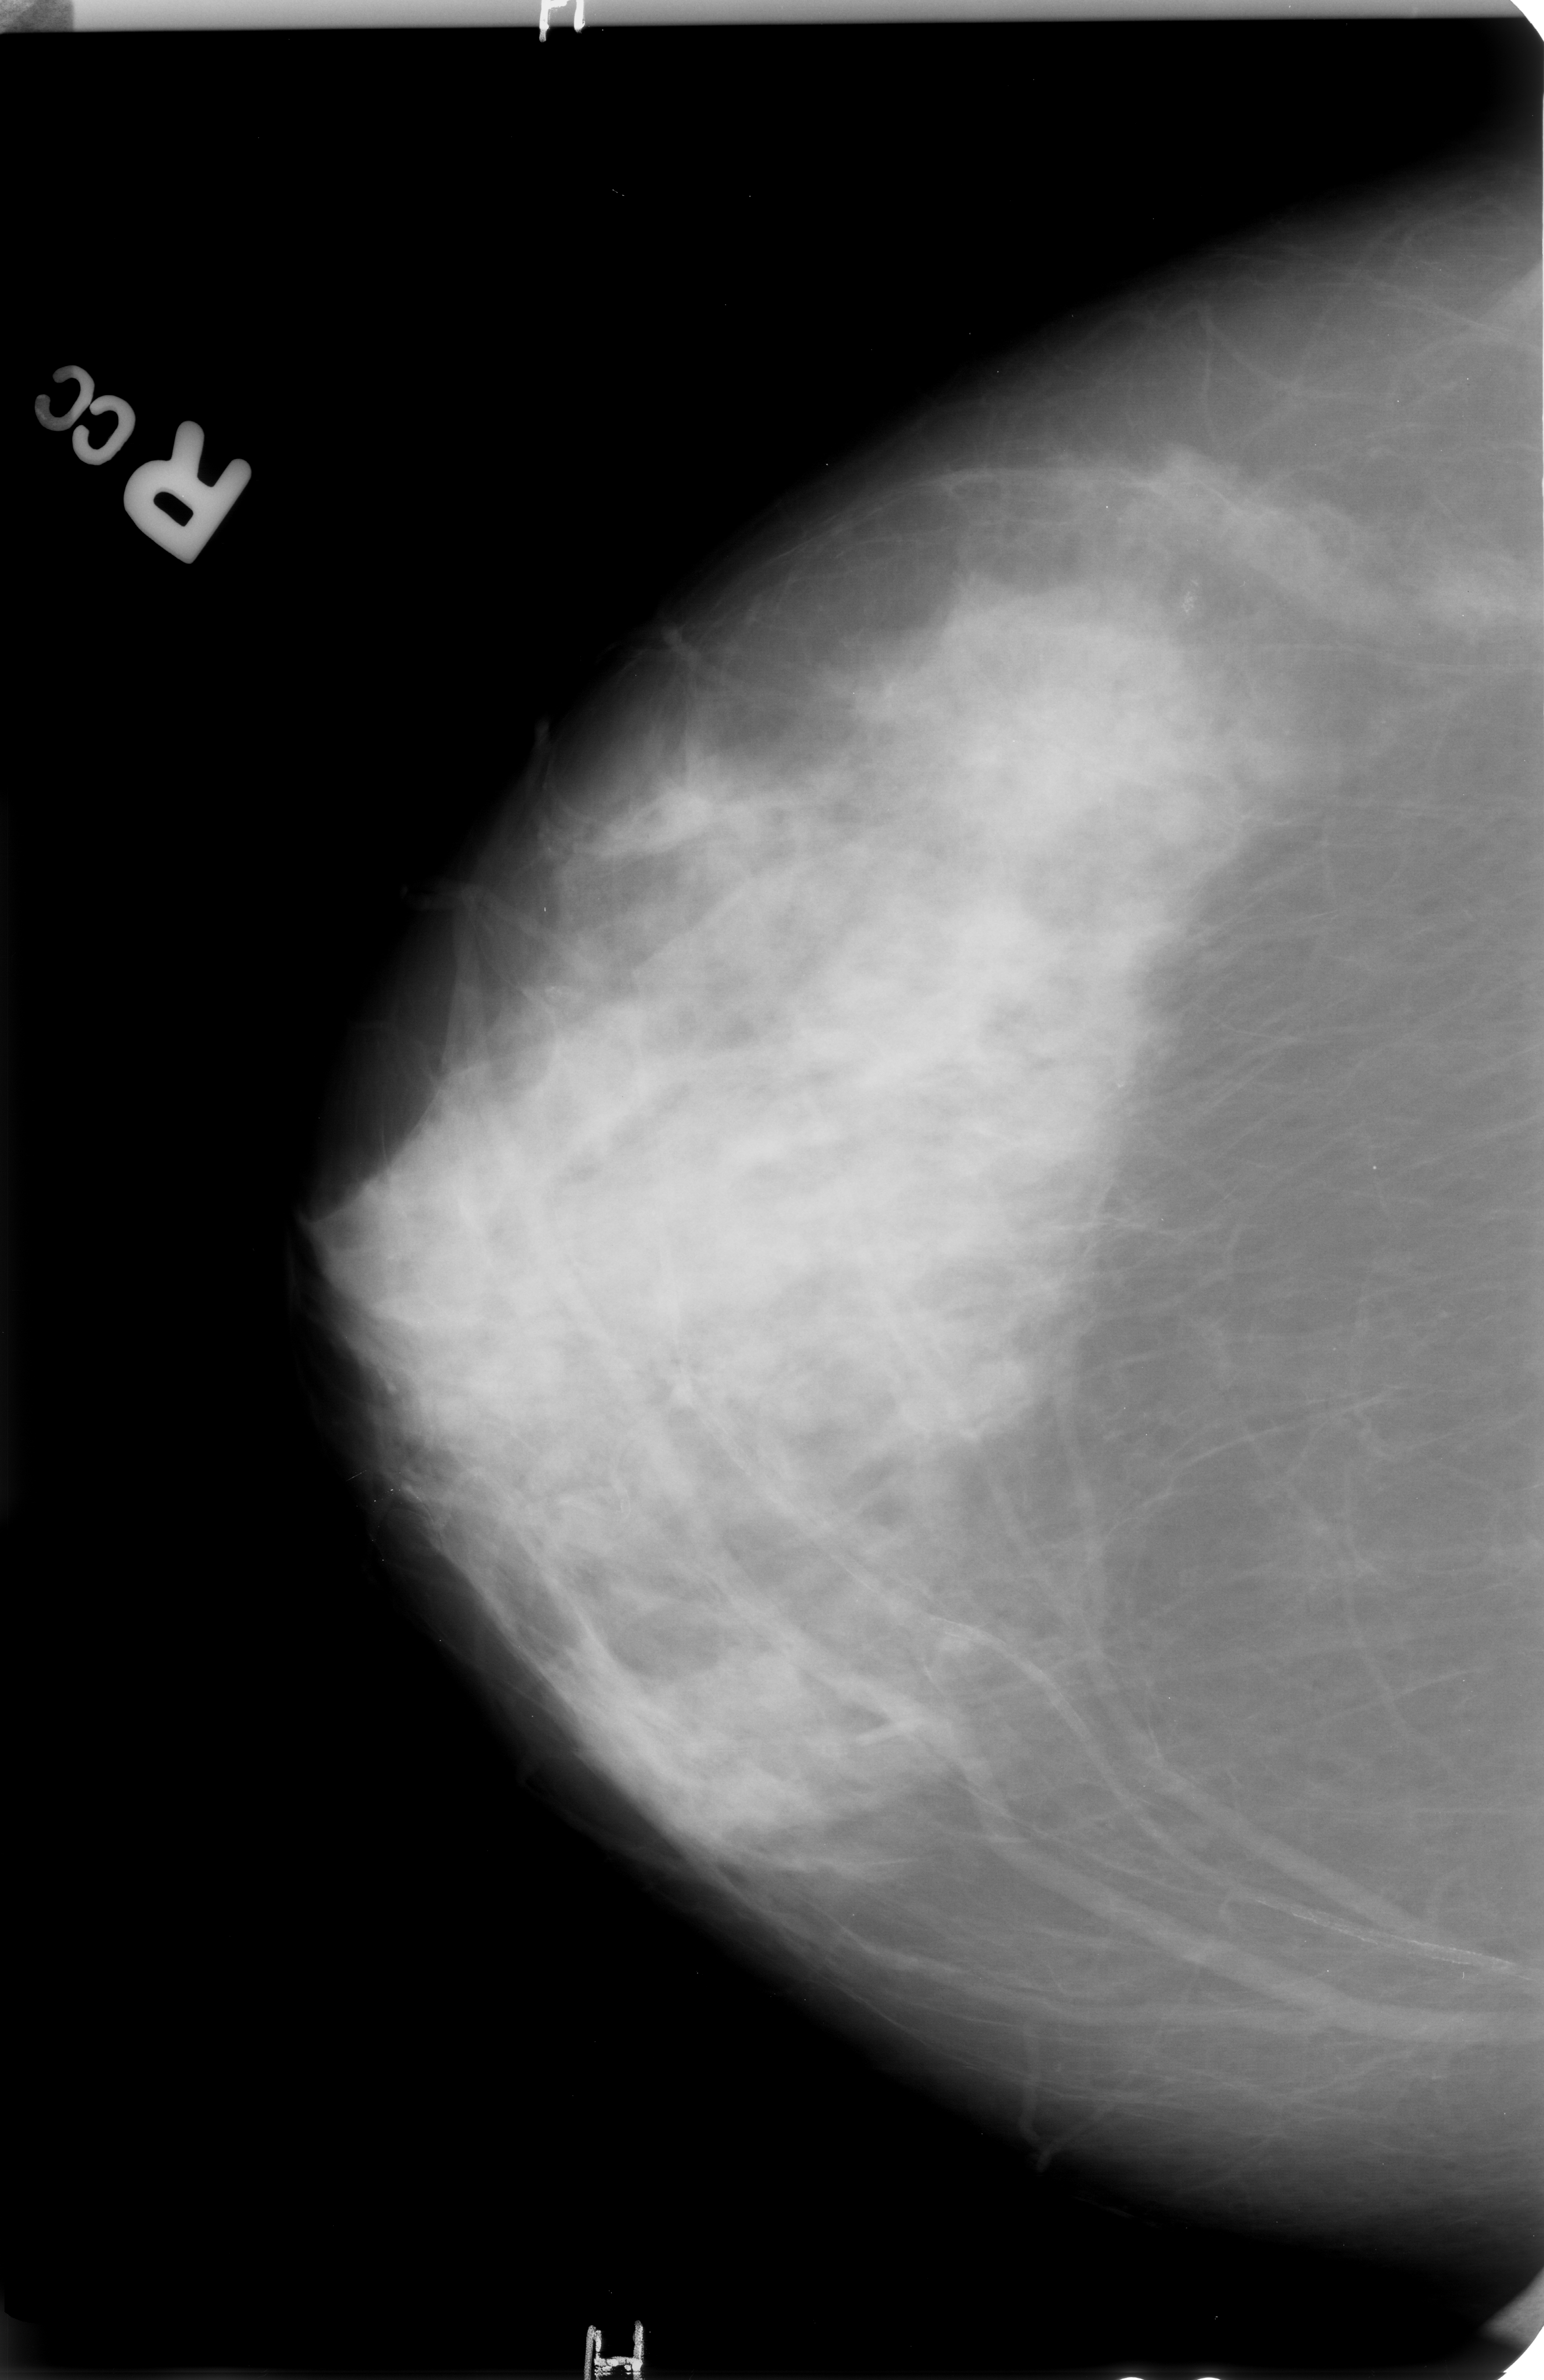
Scanned film-screen mammogram; right breast; CC view; BI-RADS breast density category 3 (scale 1–4); 1544 × 2380 image matrix.
Marked abnormalities (boxes around the expert regions of interest):
- calcifications, morphology pleomorphic, distribution clustered; BI-RADS assessment category 4; pathology result (as recorded, not read from the image): benign: box from (x=1136, y=552) to (x=1233, y=661) px